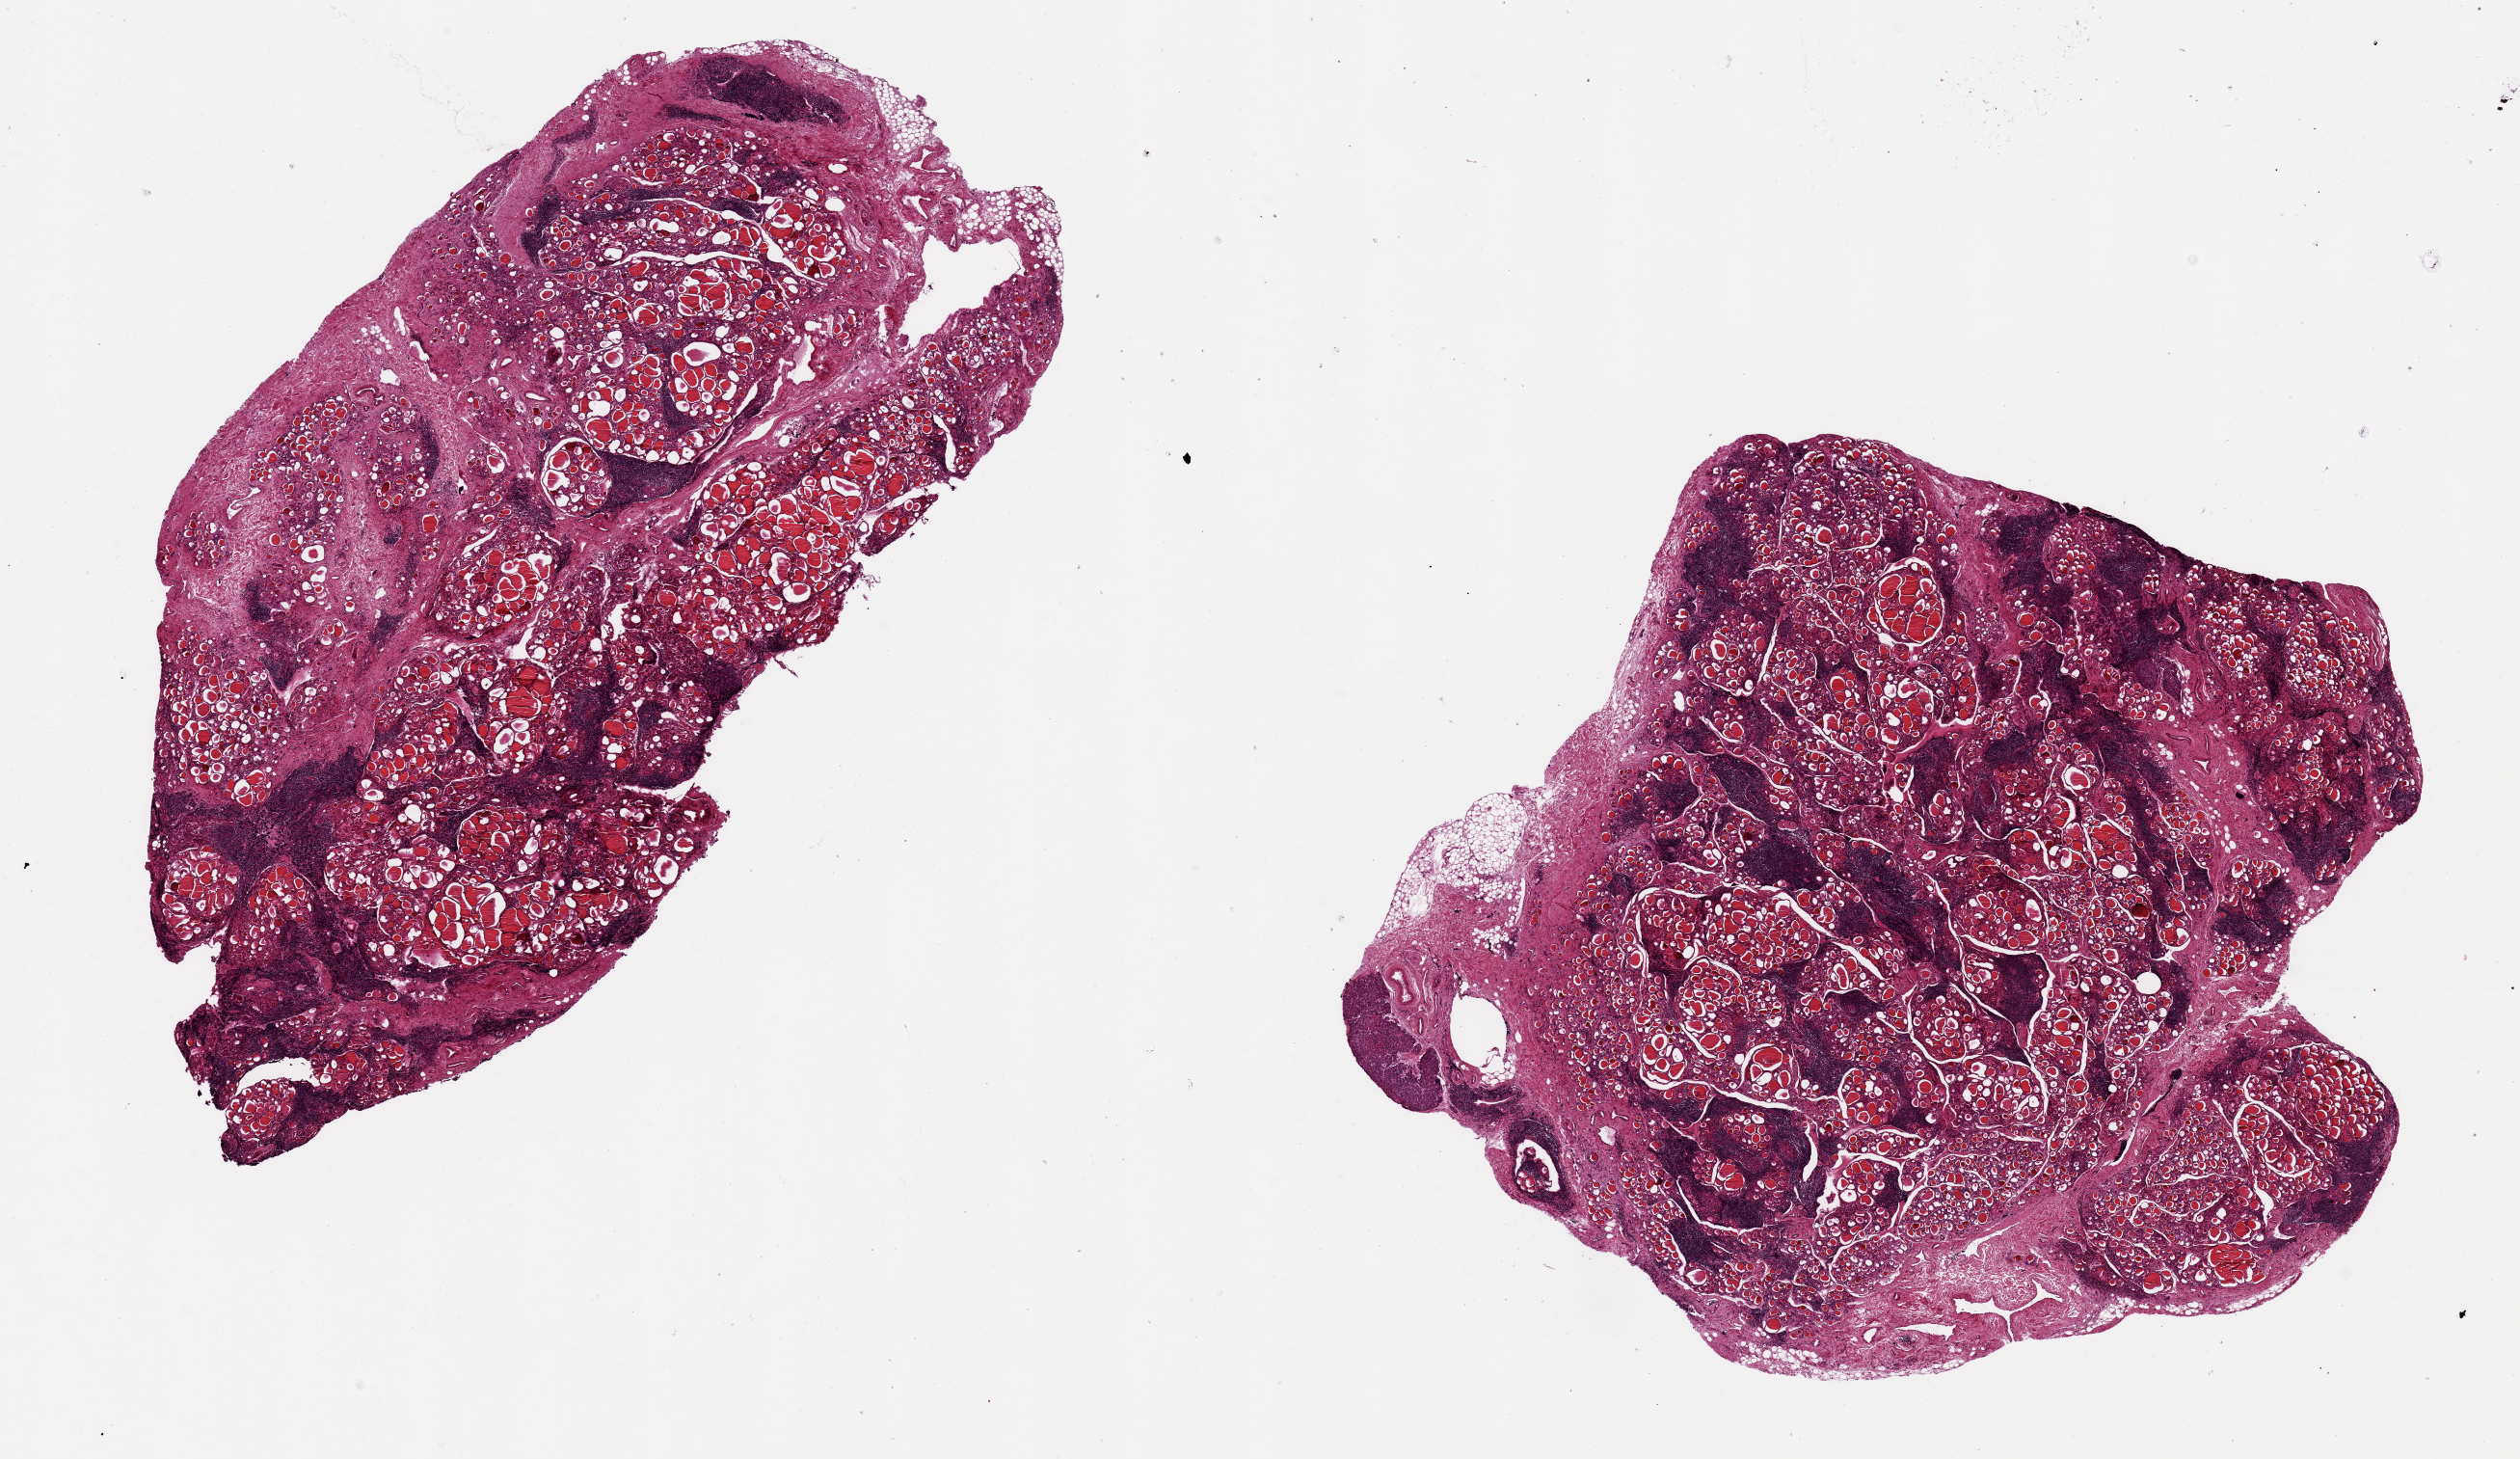
Whole-slide image, H&E stain, brightfield — whole scanned area (about 20.7 x 12.0 mm, from a 20x scan) shown as a low-resolution overview; PAXgene-fixed paraffin-embedded (PFPE) section; section of thyroid (target tissue); tissue donor sample. Female donor.
Pathologist's review note for this sample: 2 ~7x6mm pieces; Diffuse Hashimoto'sthyroiditis with regression and fibrotic areas; Representative lymphoid aggregates.